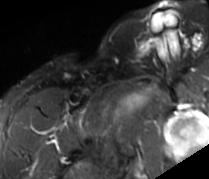
MRI of an extremity soft-tissue mass, one axial slice. Slice 78 of 89 in the series (ordered by position). STIR. MR volume resampled by the dataset authors to the PET/CT grid (not the native acquisition matrix). 3.27 mm slice thickness. 209 × 179 image matrix. Male patient. From the clinical record (not read from this slice): histological type: undifferentiated - pleiomorphic; grade: high; site of the primary tumour: right thigh.
Annotated regions visible in this slice (expert contour drawn on MRI and transferred to this co-registered scan by the dataset authors):
- gross tumour volume including surrounding oedema: bounding box [x1, y1, x2, y2] px = [114, 85, 154, 115]
- gross tumour volume (mass): [117, 96, 141, 113]